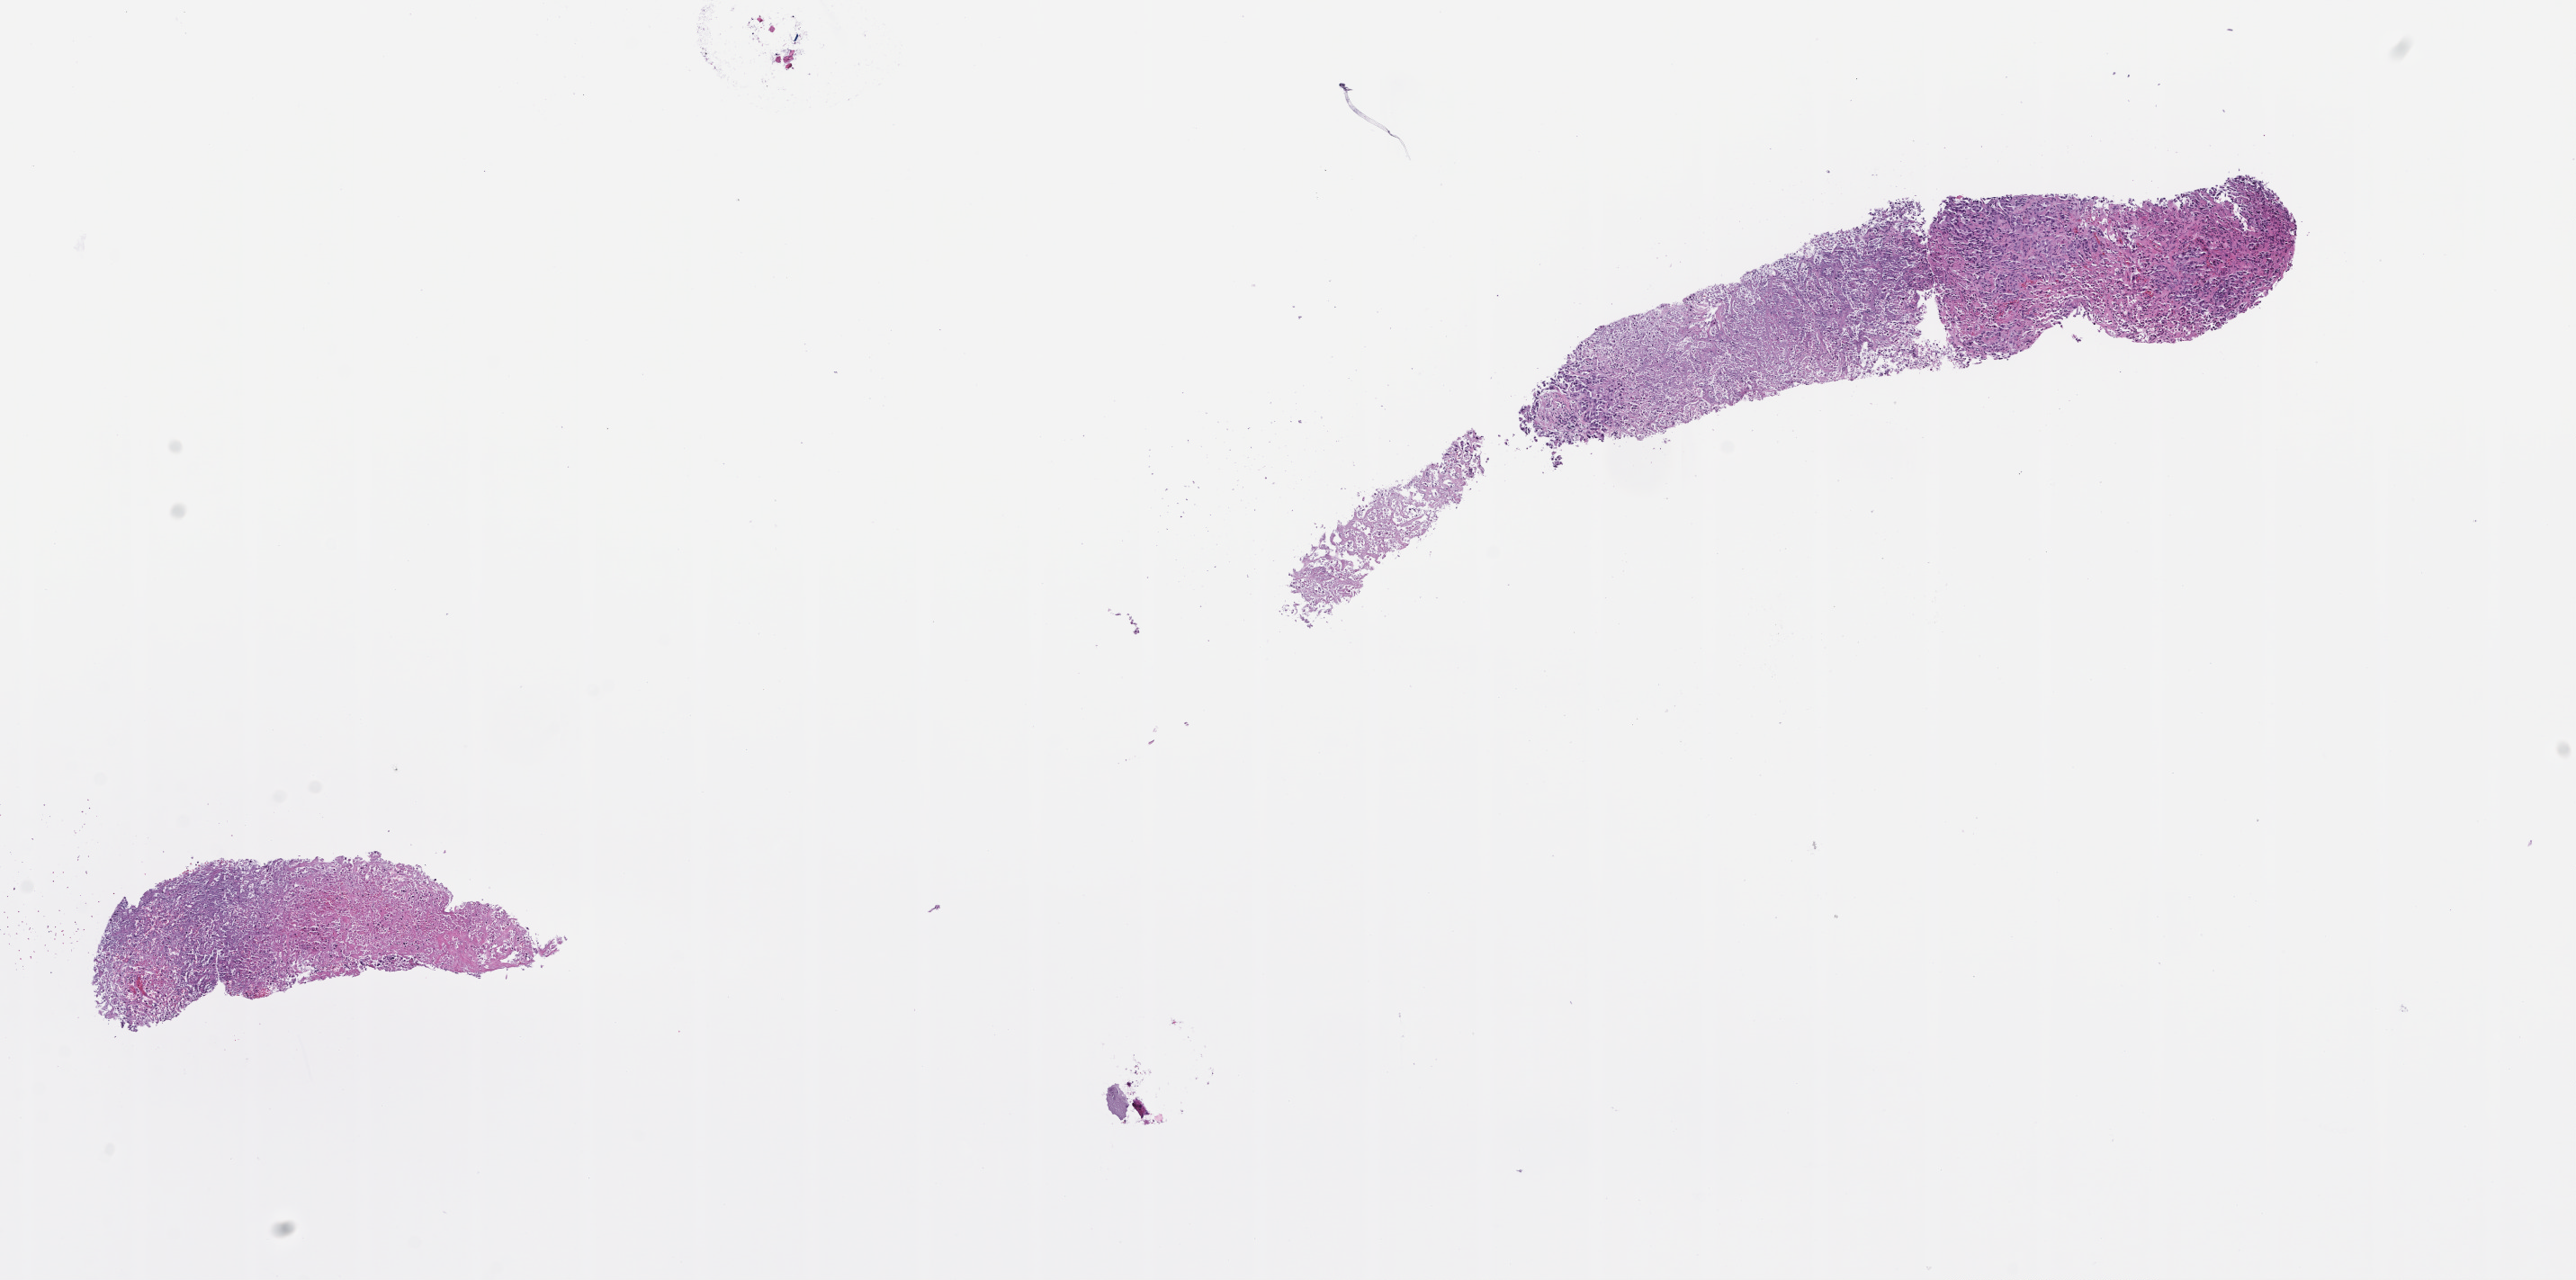
Hematoxylin and eosin (H&E) whole-slide image — shown as a low-resolution overview of the whole scanned area (about 11.6 x 5.7 mm); formalin-fixed, paraffin-embedded (FFPE) tissue; specimen time point: collected at baseline (before treatment). Male patient.
This section: metastatic tumor tissue. Primary diagnosis of the patient: Non-Small Cell Lung Carcinoma.